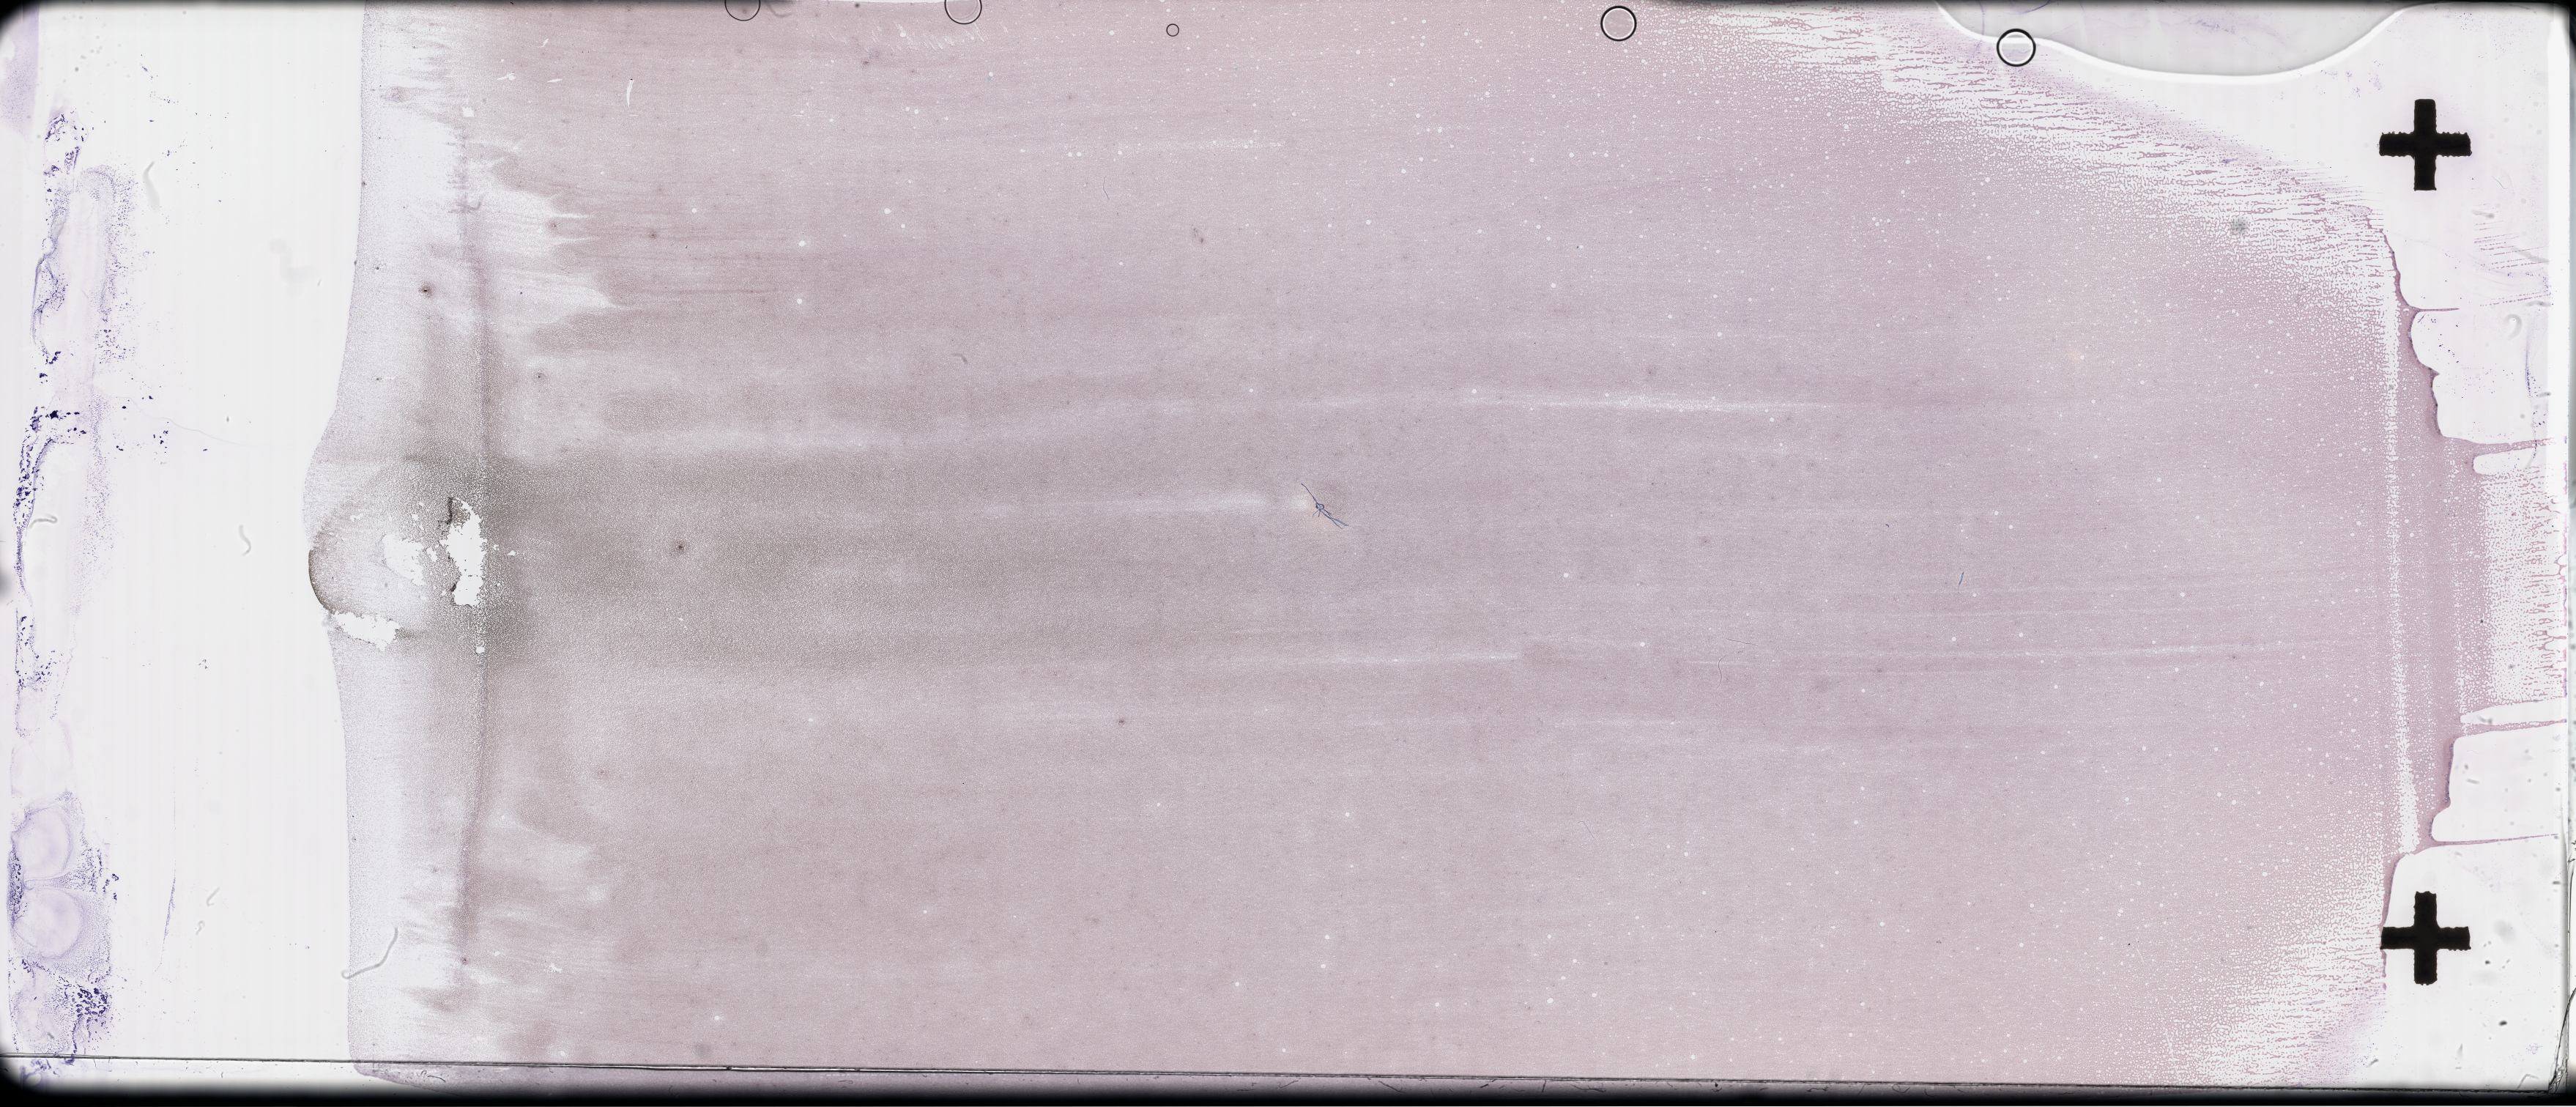
Whole-slide image of a whole blood smear, Wright-Giemsa stain — shown as a low-resolution overview of the whole scanned area (about 56.8 x 24.4 mm); collected at disease progression. Female patient.
• from a patient with: Plasma Cell Myeloma